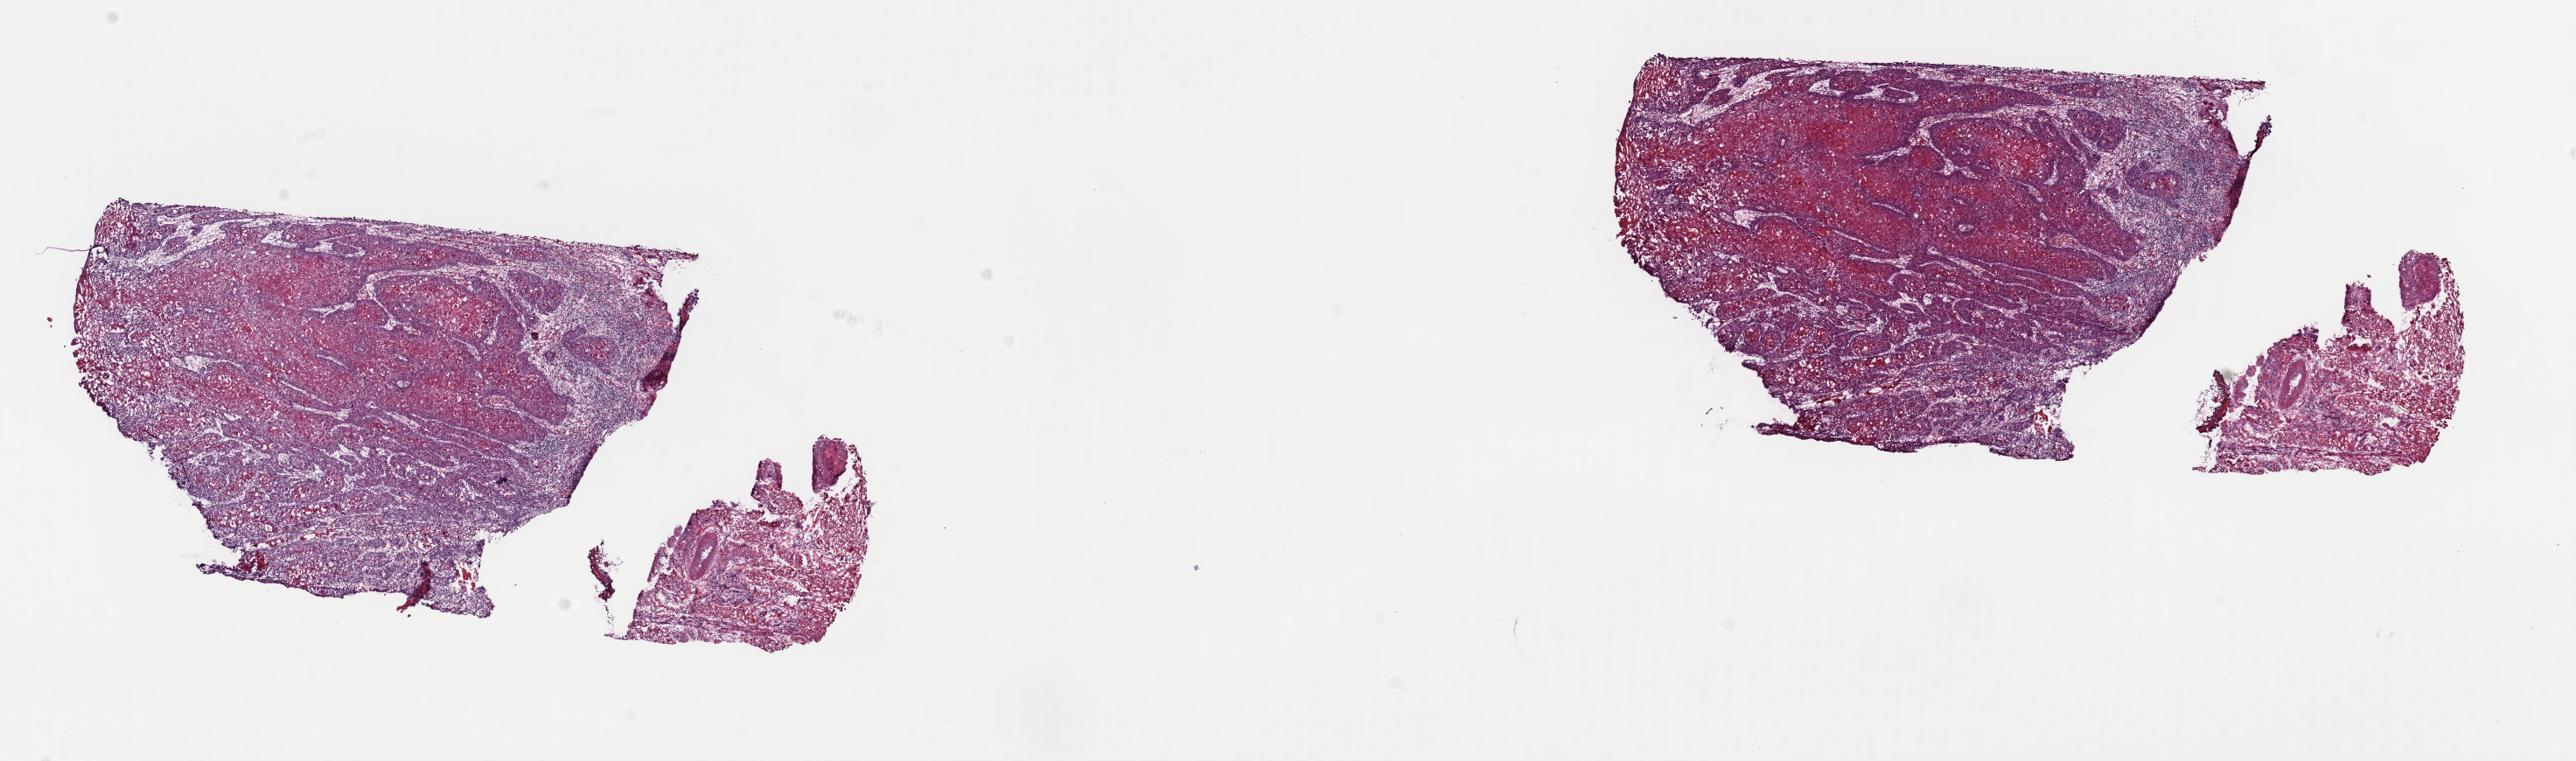
Digitized Hematoxylin and eosin (H&E) stained tissue section (whole slide) — a low-resolution overview of the entire scanned area, about 23.3 x 6.9 mm (slide scanned at 40x), frozen section from the top of the tissue portion, head and neck, primary tumour sample. Male patient. Histologic grade: G2 (moderately differentiated). Pathologist review of this section (percent, as recorded): tumour cells 80%, tumour nuclei 80%, normal cells 0%, stromal cells 20%, necrosis 0%. Inflammatory infiltration, as recorded: lymphocyte infiltration 100%, monocyte infiltration 0%, neutrophil infiltration 0%.
AJCC pathologic stage: II. TNM: T2 N0 M0. Lymph nodes positive (case pathology): 0 of 25 examined. Histologic diagnosis: Squamous cell carcinoma, NOS (ventral surface of tongue, NOS). Laterality: left.